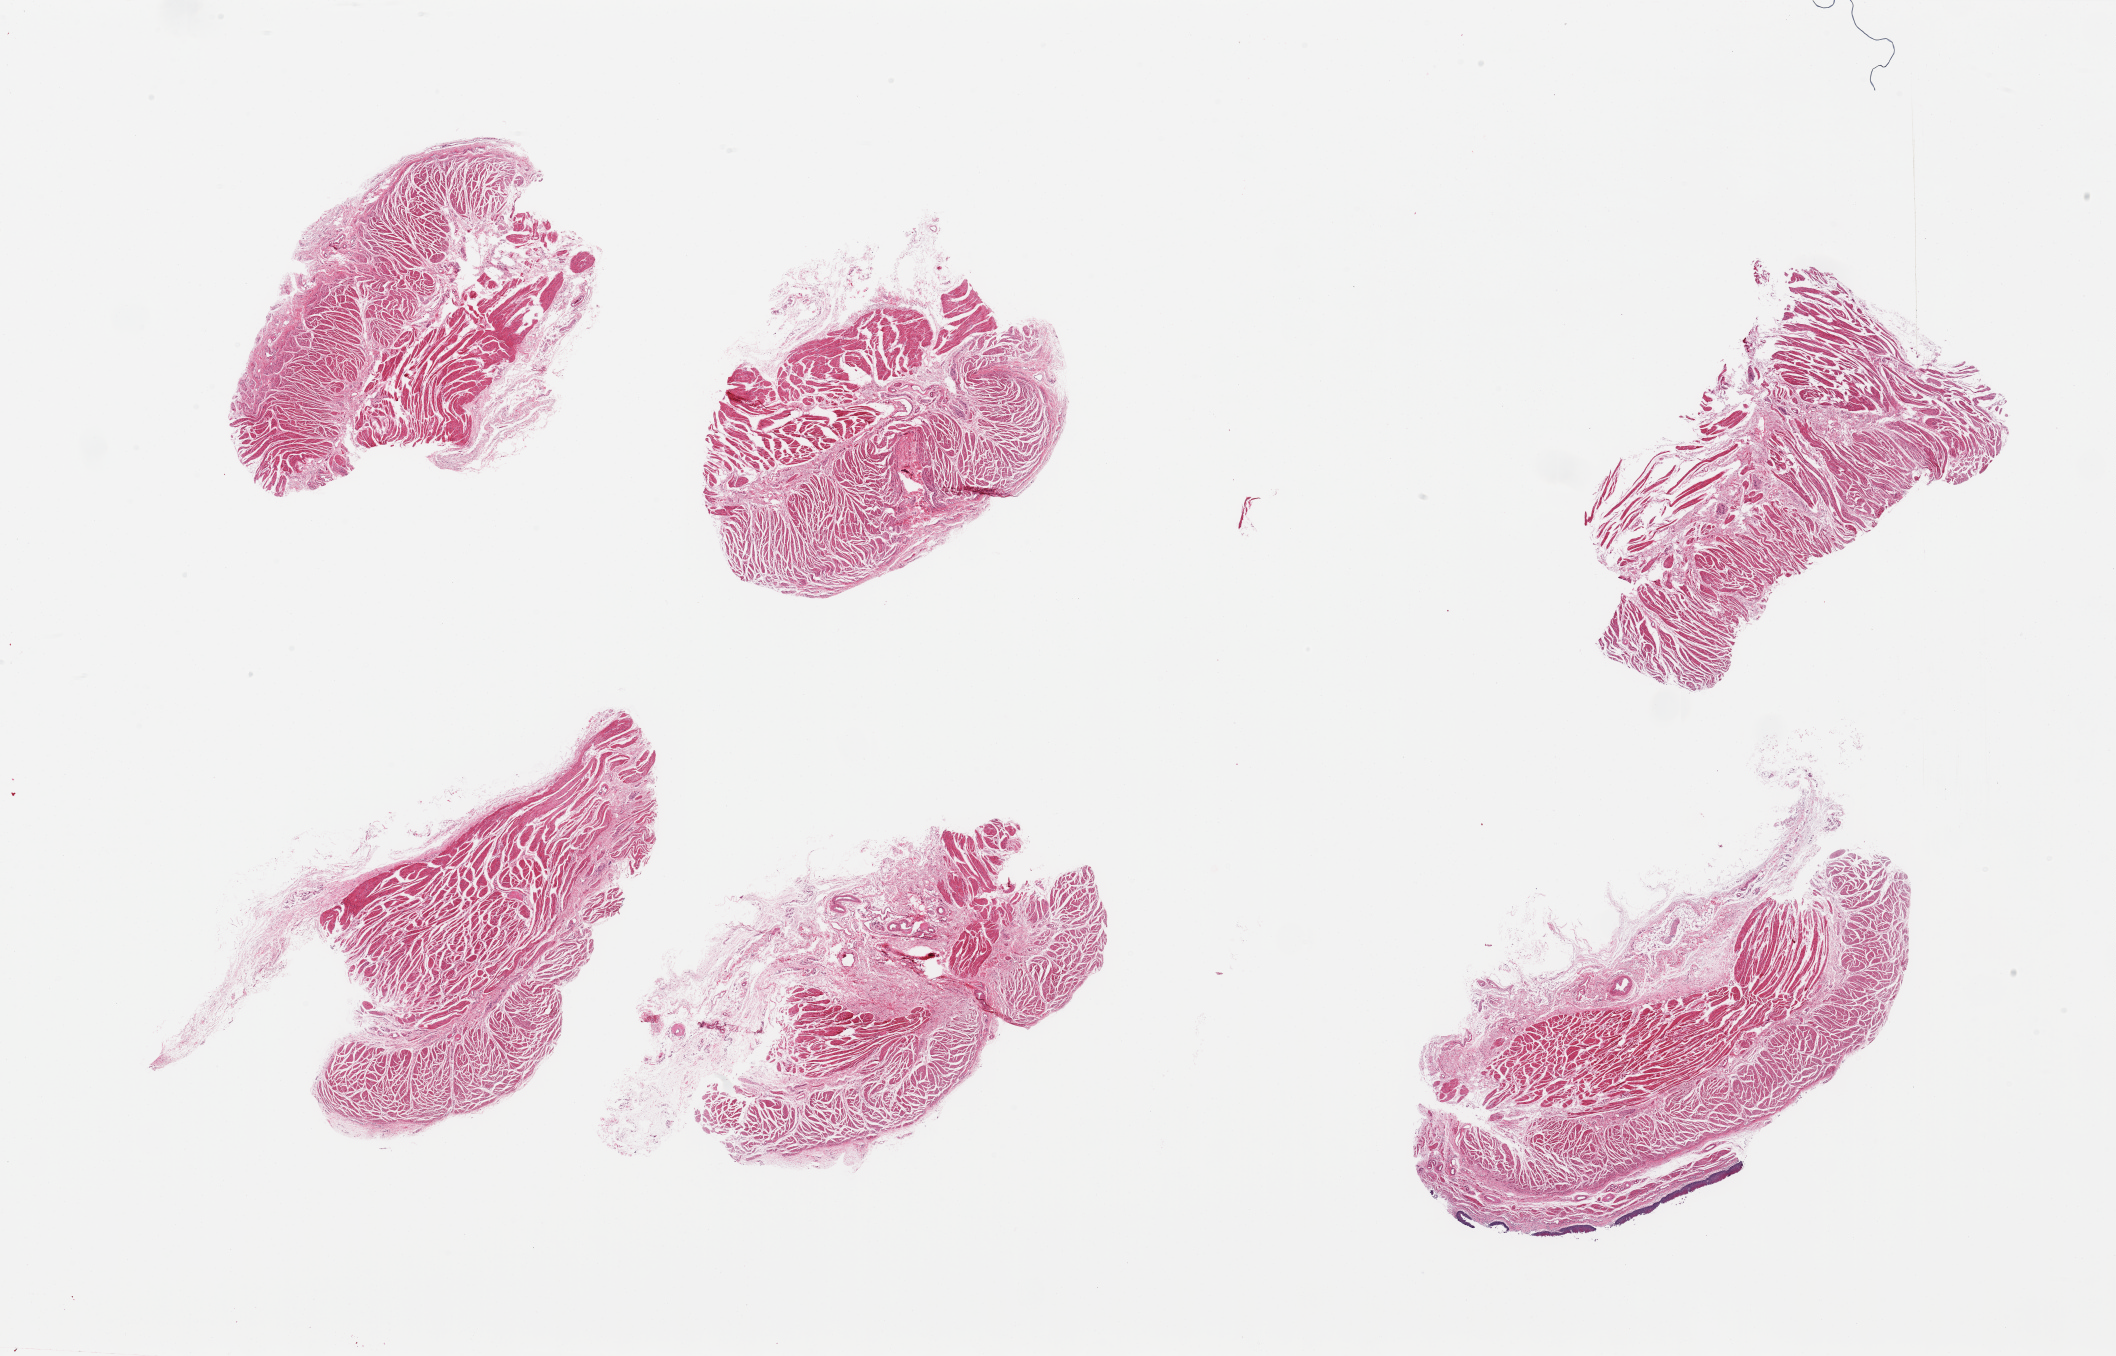
Whole-slide image, hematoxylin and eosin (H&E) stain, whole scanned area (about 33.5 x 21.4 mm, from a 20x scan) shown as a low-resolution overview; PAXgene-fixed, paraffin-embedded tissue; target tissue: gastroesophageal junction; tissue donor sample. Donor: female.
Review note (as recorded): 6 pieces; 1 of 6 has squamous mucosa on surface, 10% of content.